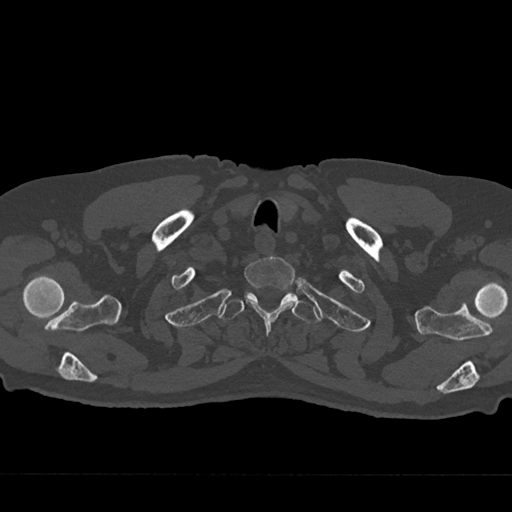
CT including the spine, one axial slice; position 637 of 797 along the scan axis; reconstruction kernel Br40s/3; bone window (W 1800 / L 400 HU); 0.5 mm slice thickness; 512 × 512 image matrix. Patient: male, 75 years. Case-level facts recorded for this patient, not image findings: primary cancer: renal.
Annotated regions visible in this slice (semi-automatically segmented with operator editing):
- T1 vertebra: box from (x=244, y=257) to (x=296, y=335) px
- T2 vertebra: (x=218, y=292)–(x=320, y=324)